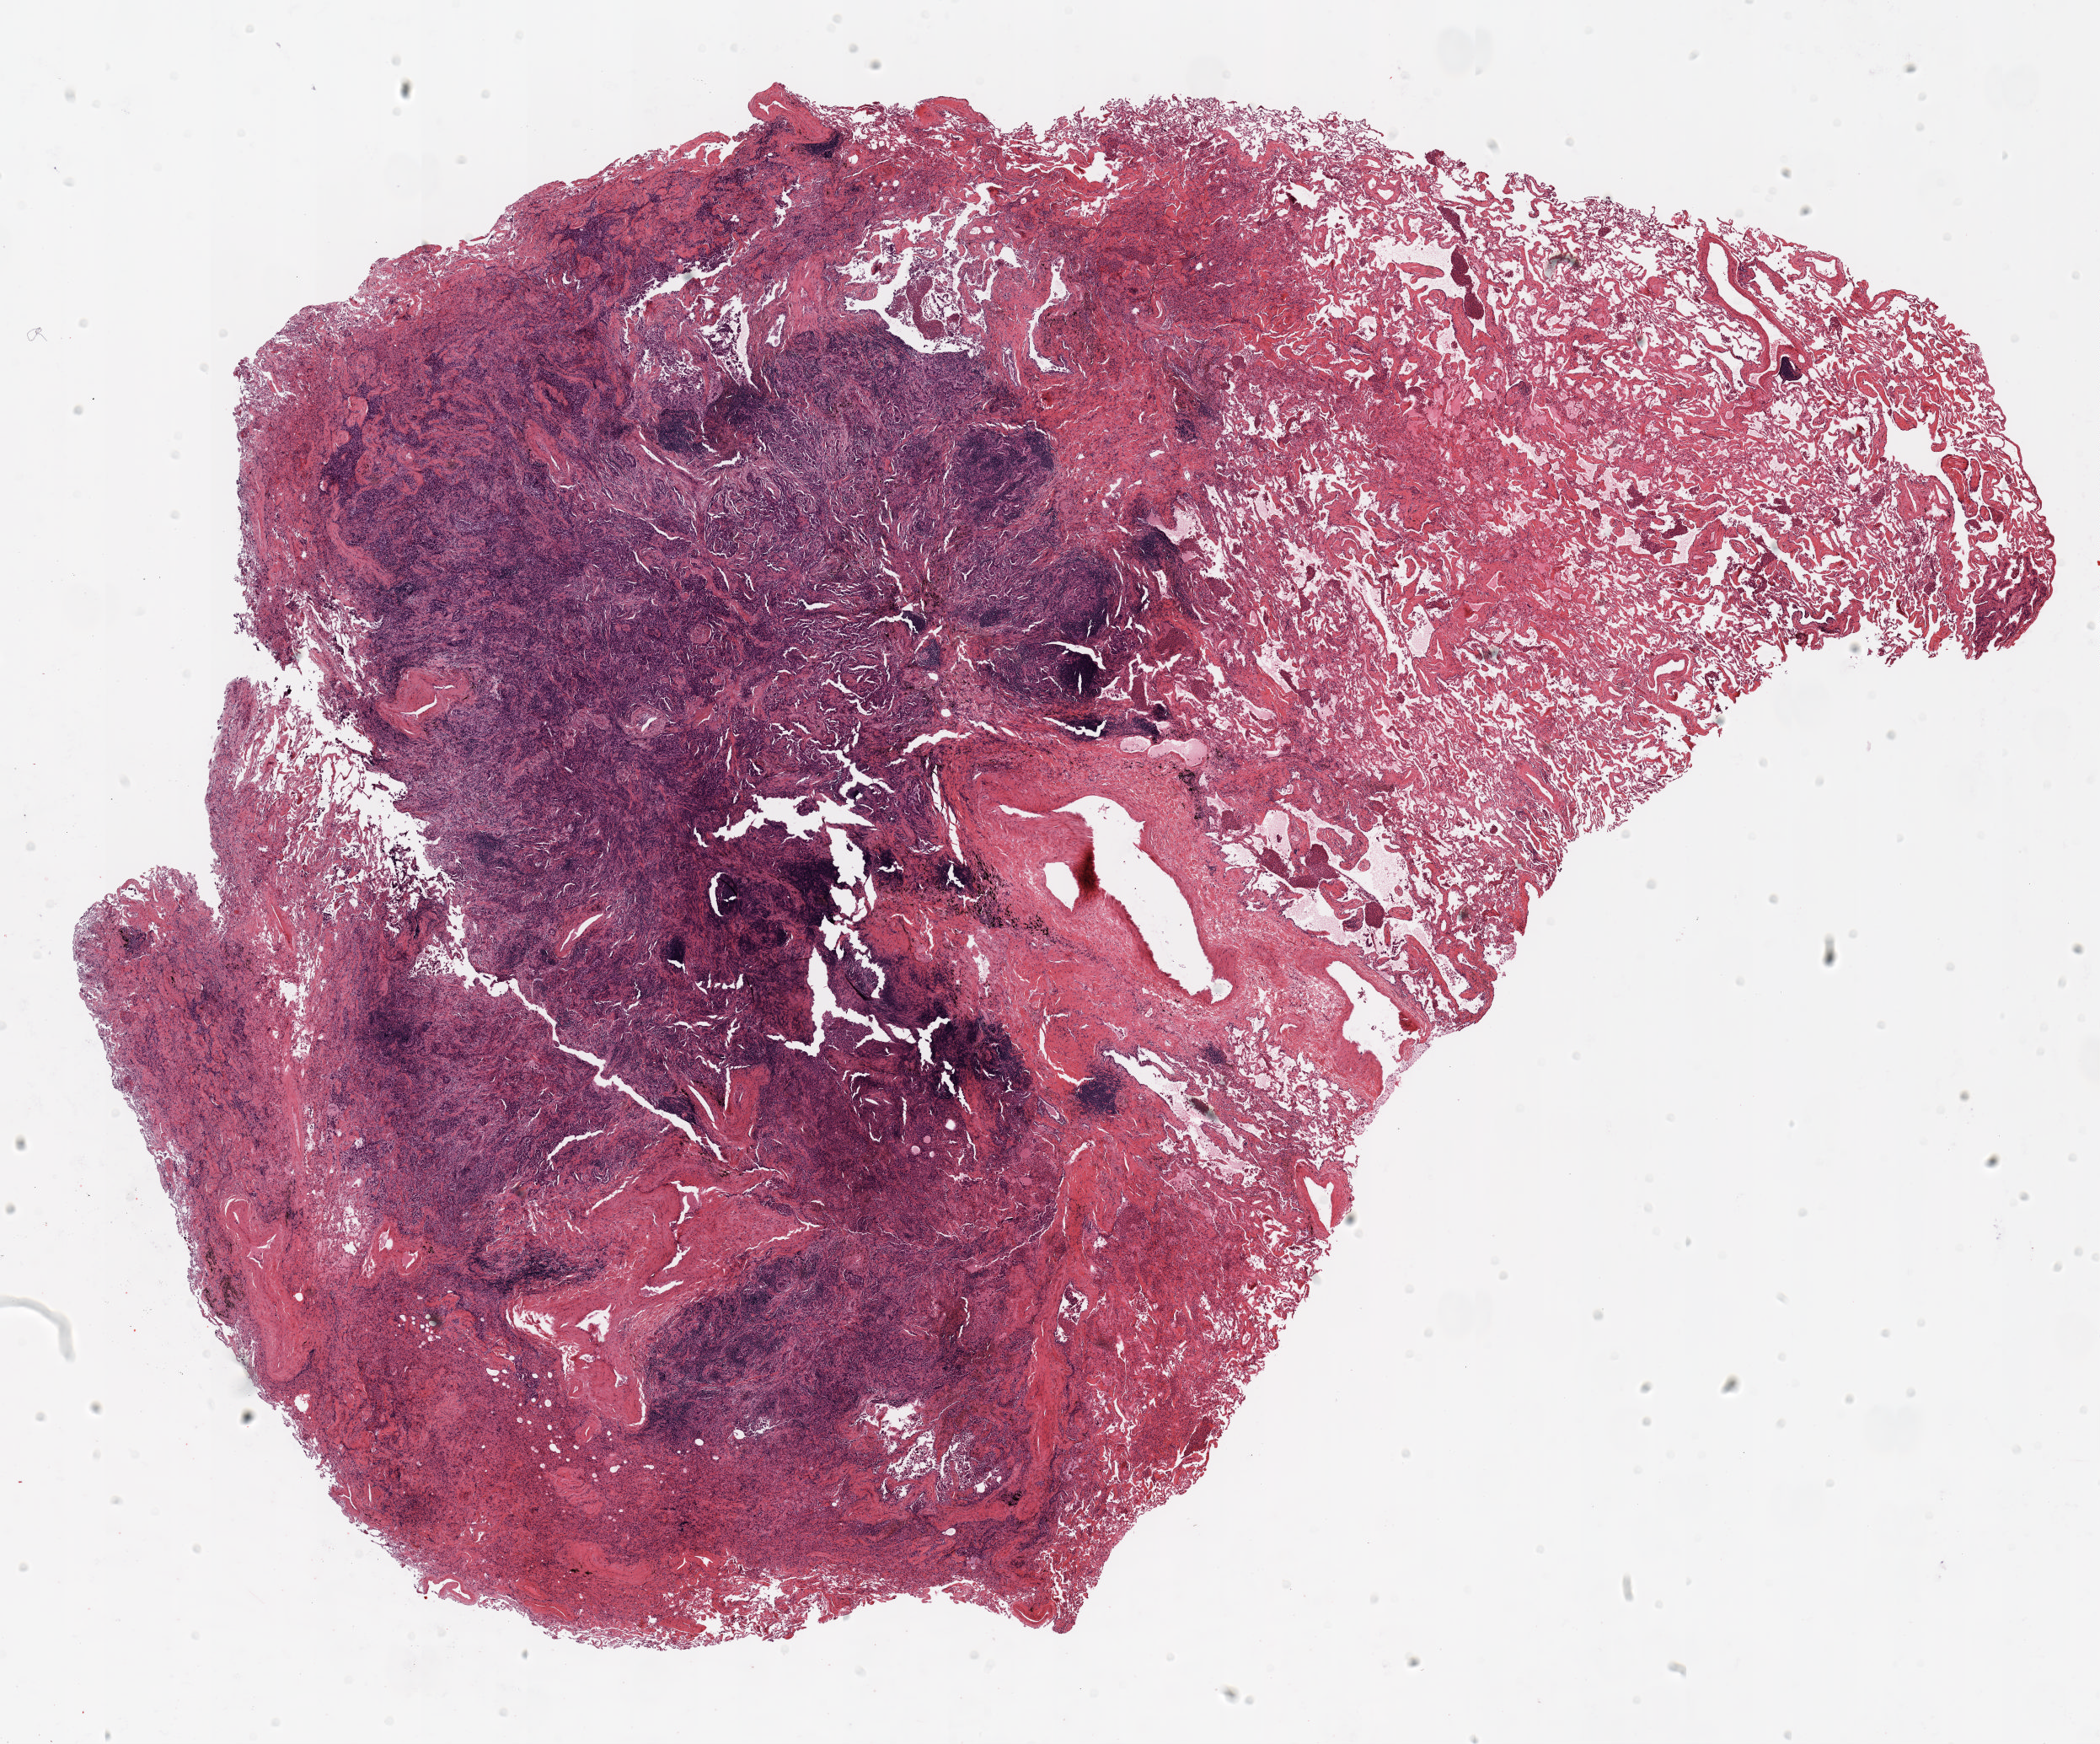
Whole-slide histology image, Hematoxylin and eosin (H&E) stained, whole scanned area (about 20.0 x 16.6 mm, acquisition: 20x scan) shown as a low-resolution overview. Formalin-fixed paraffin-embedded (FFPE) section. Lung tissue. Female, age 60 at enrolment. Current smoker at enrolment. Grade: poorly differentiated (G3).
• primary tumour location (clinical record): left upper lobe
• tumour size (pathology): 10 mm
• stage (AJCC 6th edition): IA
• participant's lung-cancer diagnosis: Non-small cell carcinoma